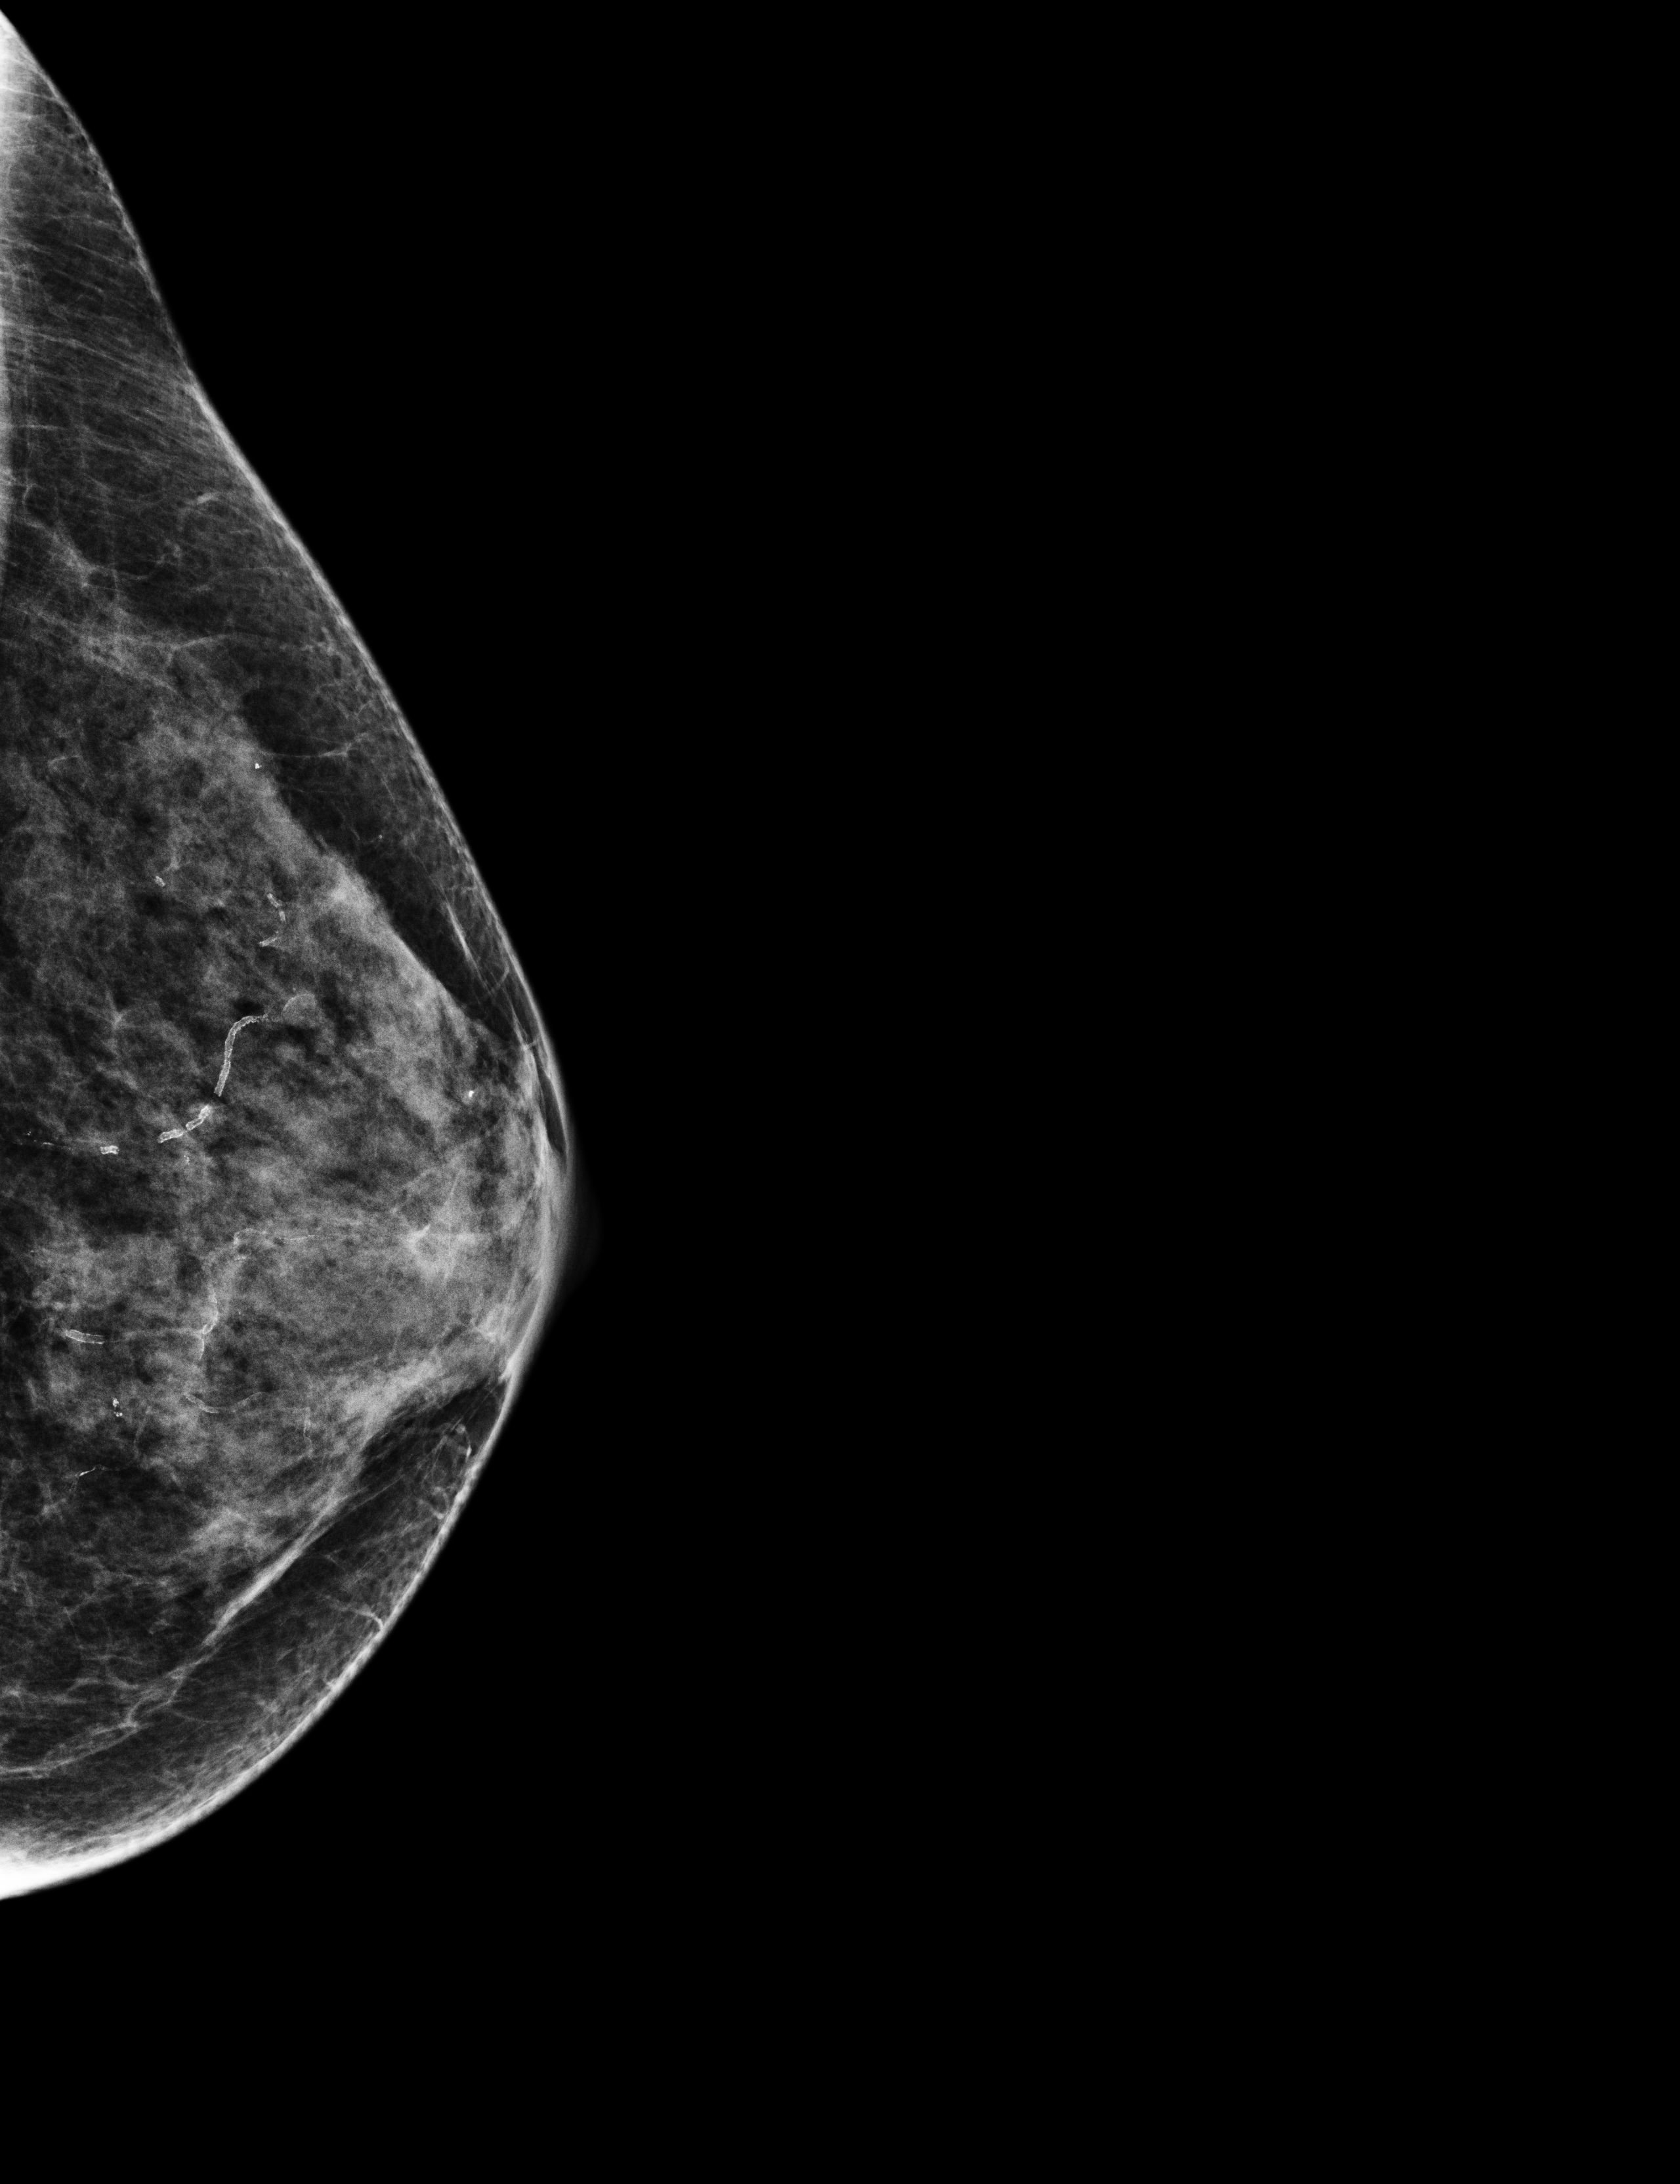
Annual screening mammography examination, compressed breast thickness 35 mm. Patient: female, 65 years.
Image type: full-field digital mammogram. Breast: left. Projection: exaggerated CC view (lateral).